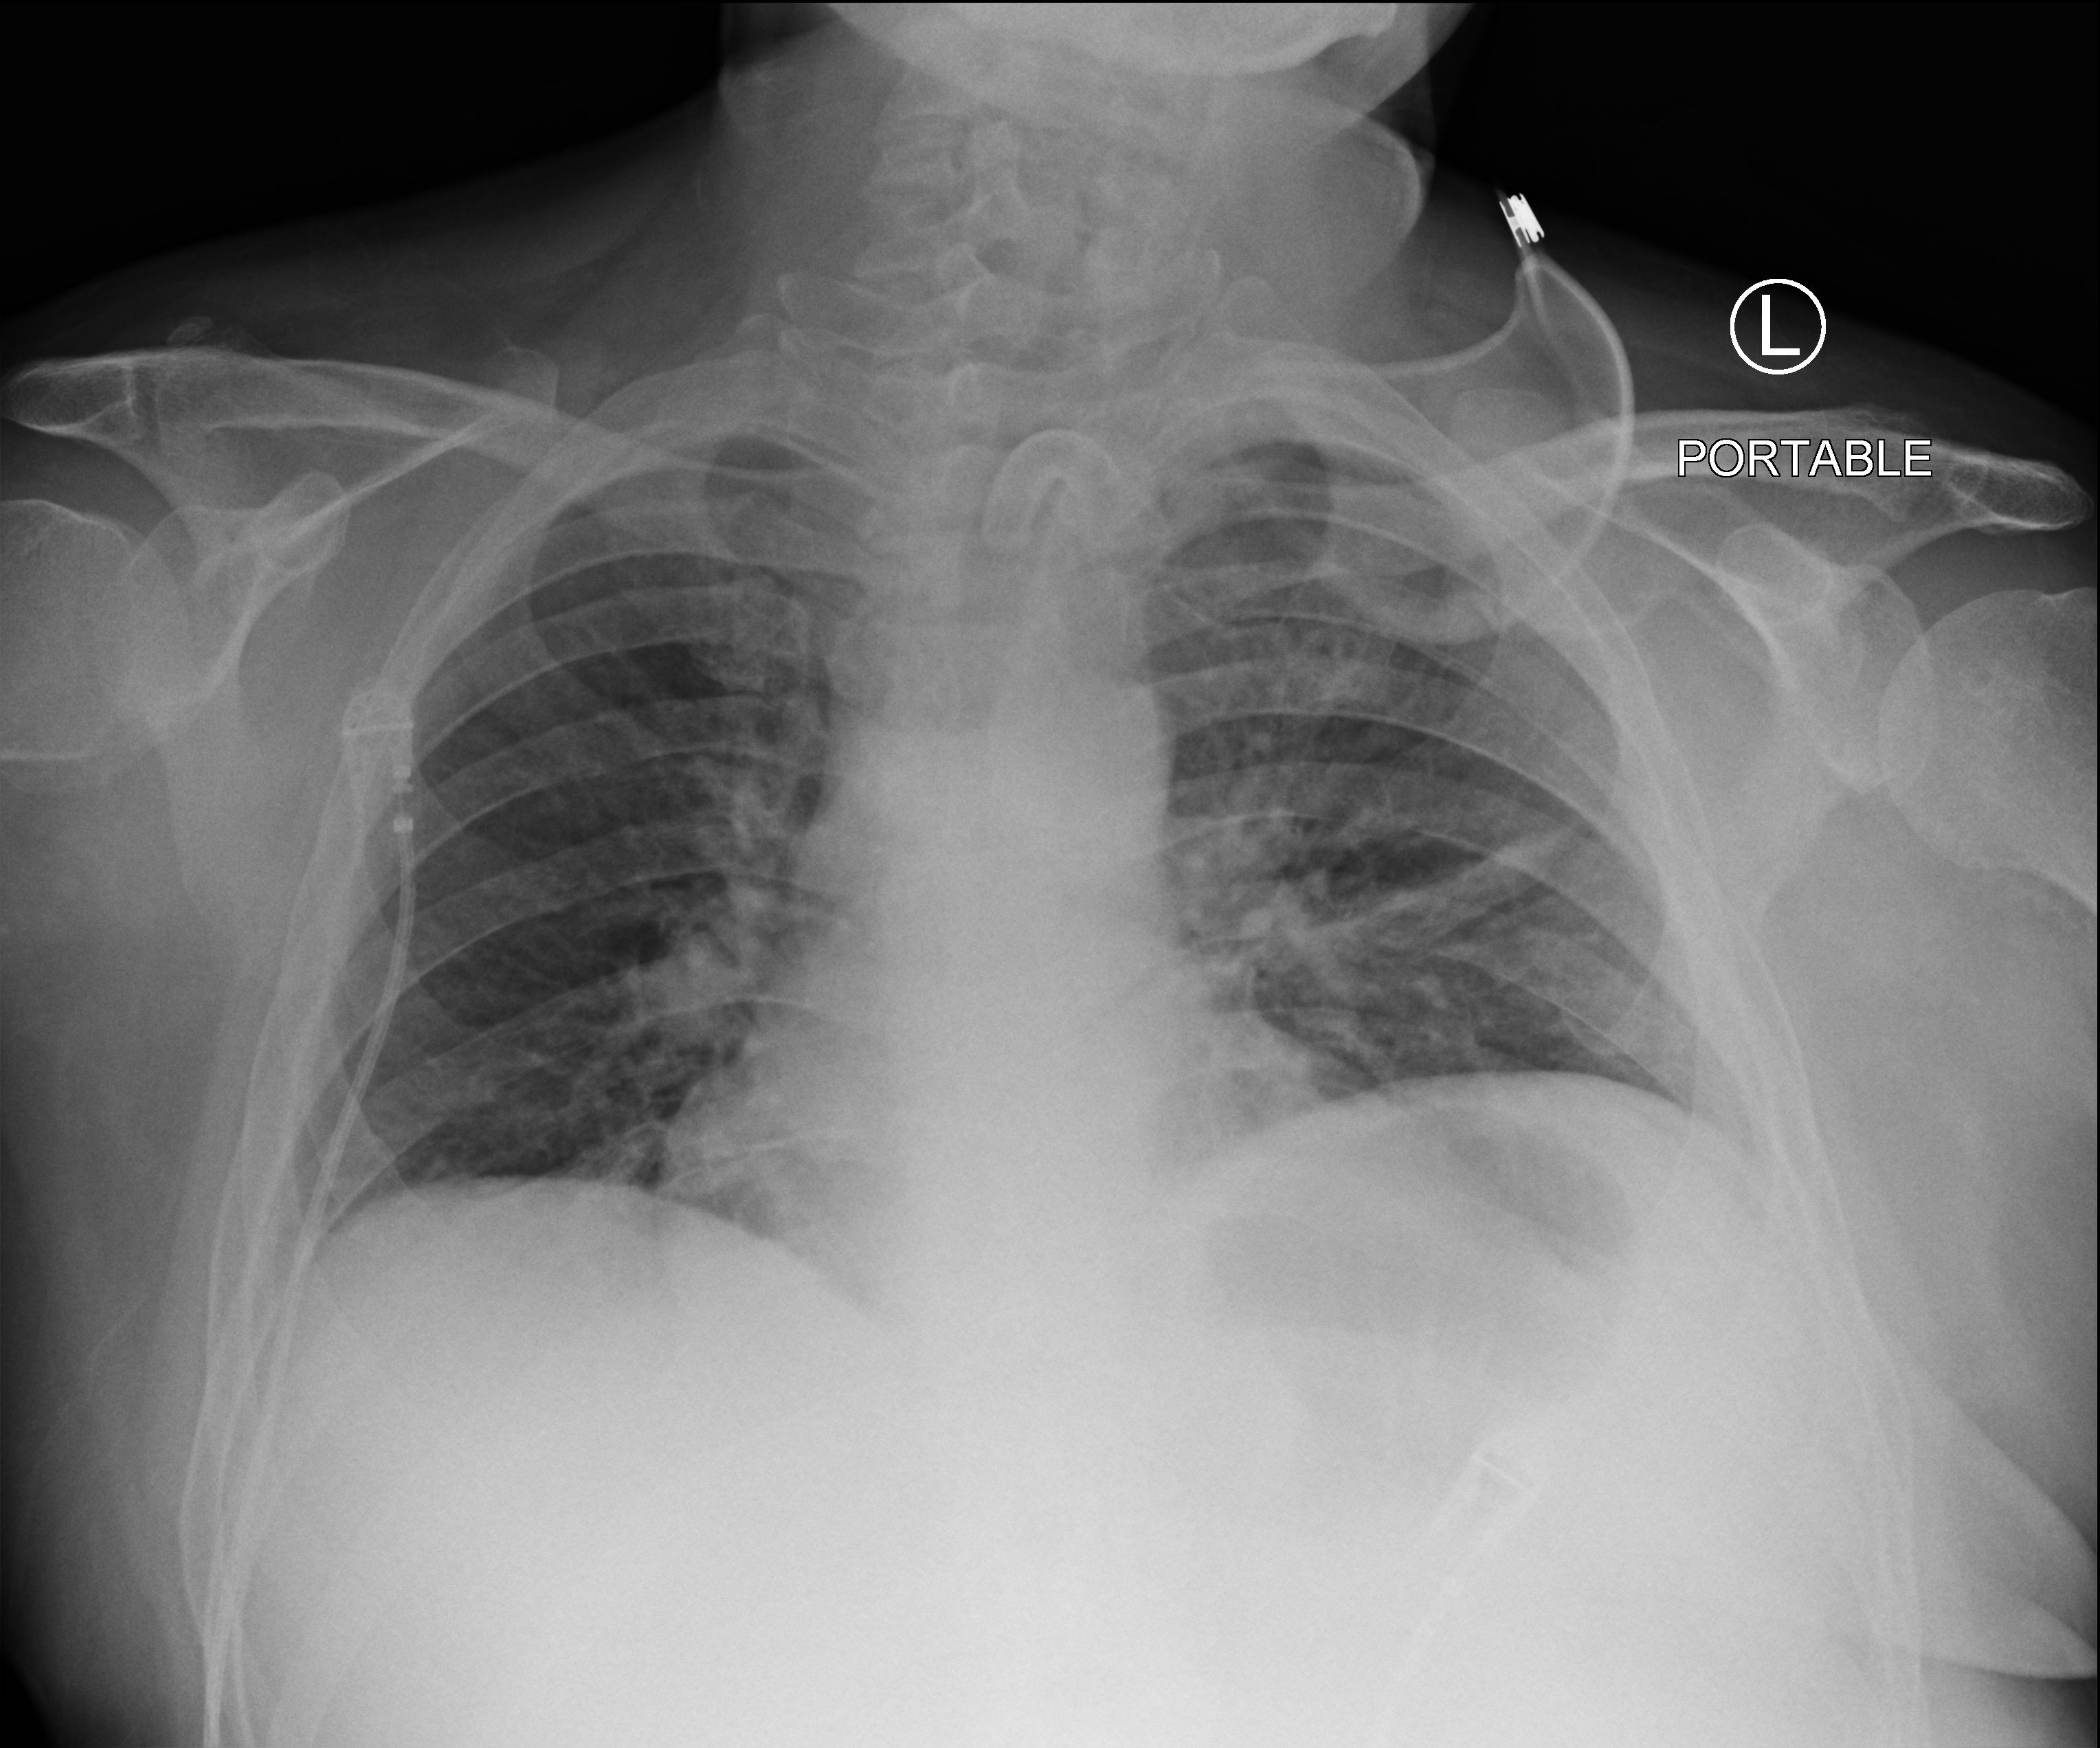
Portable chest radiograph. Patient hospitalised with COVID-19; male, aged 18–59 years.
From the hospital-stay record, not from the radiograph (when in the stay this image was taken is not recorded):
- admitted to intensive care during this hospital stay: yes
- mechanically ventilated during this hospital stay: yes